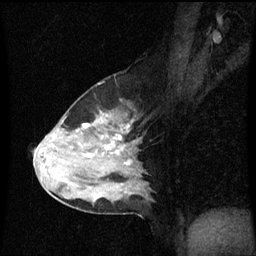
Breast MRI (dynamic contrast-enhanced), one sagittal slice. Position 38 of 60 along the scan axis. Dynamic contrast-enhanced series, image 2 of 3 at this slice position (ordered by acquisition). 1.5 T. TE 4.2 ms, TR 8.9 ms. 2 mm slice thickness. 256 × 256 image matrix. Female patient, age 50 years. From the clinical record (not read from this slice): setting: breast cancer imaged before/during neoadjuvant chemotherapy; receptor status: HR-positive, HER2-negative.
Structures marked on this image (semi-automatically segmented with operator editing):
- analysis volume of interest (the breast-tissue region the enhancement analysis was run in; not a lesion): bounding box (x1, y1, x2, y2) in pixels: (36, 96, 147, 209)
- tumour enhancement mask (voxels above the 70 % enhancement threshold inside the analysis volume of interest): (85, 114, 123, 155)